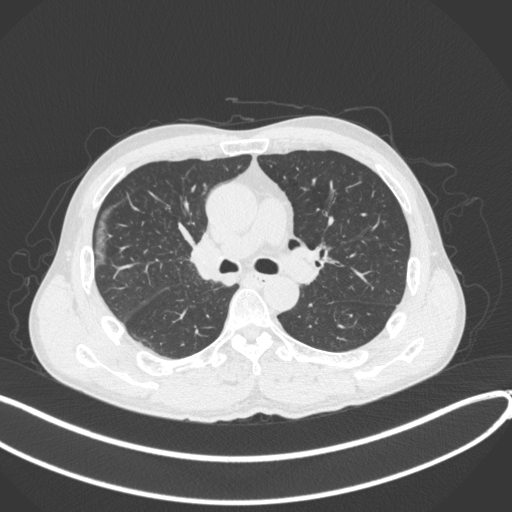
Chest CT, one axial slice. Position 236 of 409 along the scan axis. 120 kVp. Lung window (W 1500 / L -600 HU). 1 mm slice thickness. 512 × 512 image matrix, field of view 400 × 400 mm. Patient: male, 53 years. From the clinical record (not read from this slice): clinical TNM (as recorded): T1b N0 M0.
Annotated regions visible in this slice (bounding box drawn by a radiologist):
- lung tumour (recorded histology: squamous cell carcinoma): bounding box (x1, y1, x2, y2) in pixels: (184, 231, 225, 288)